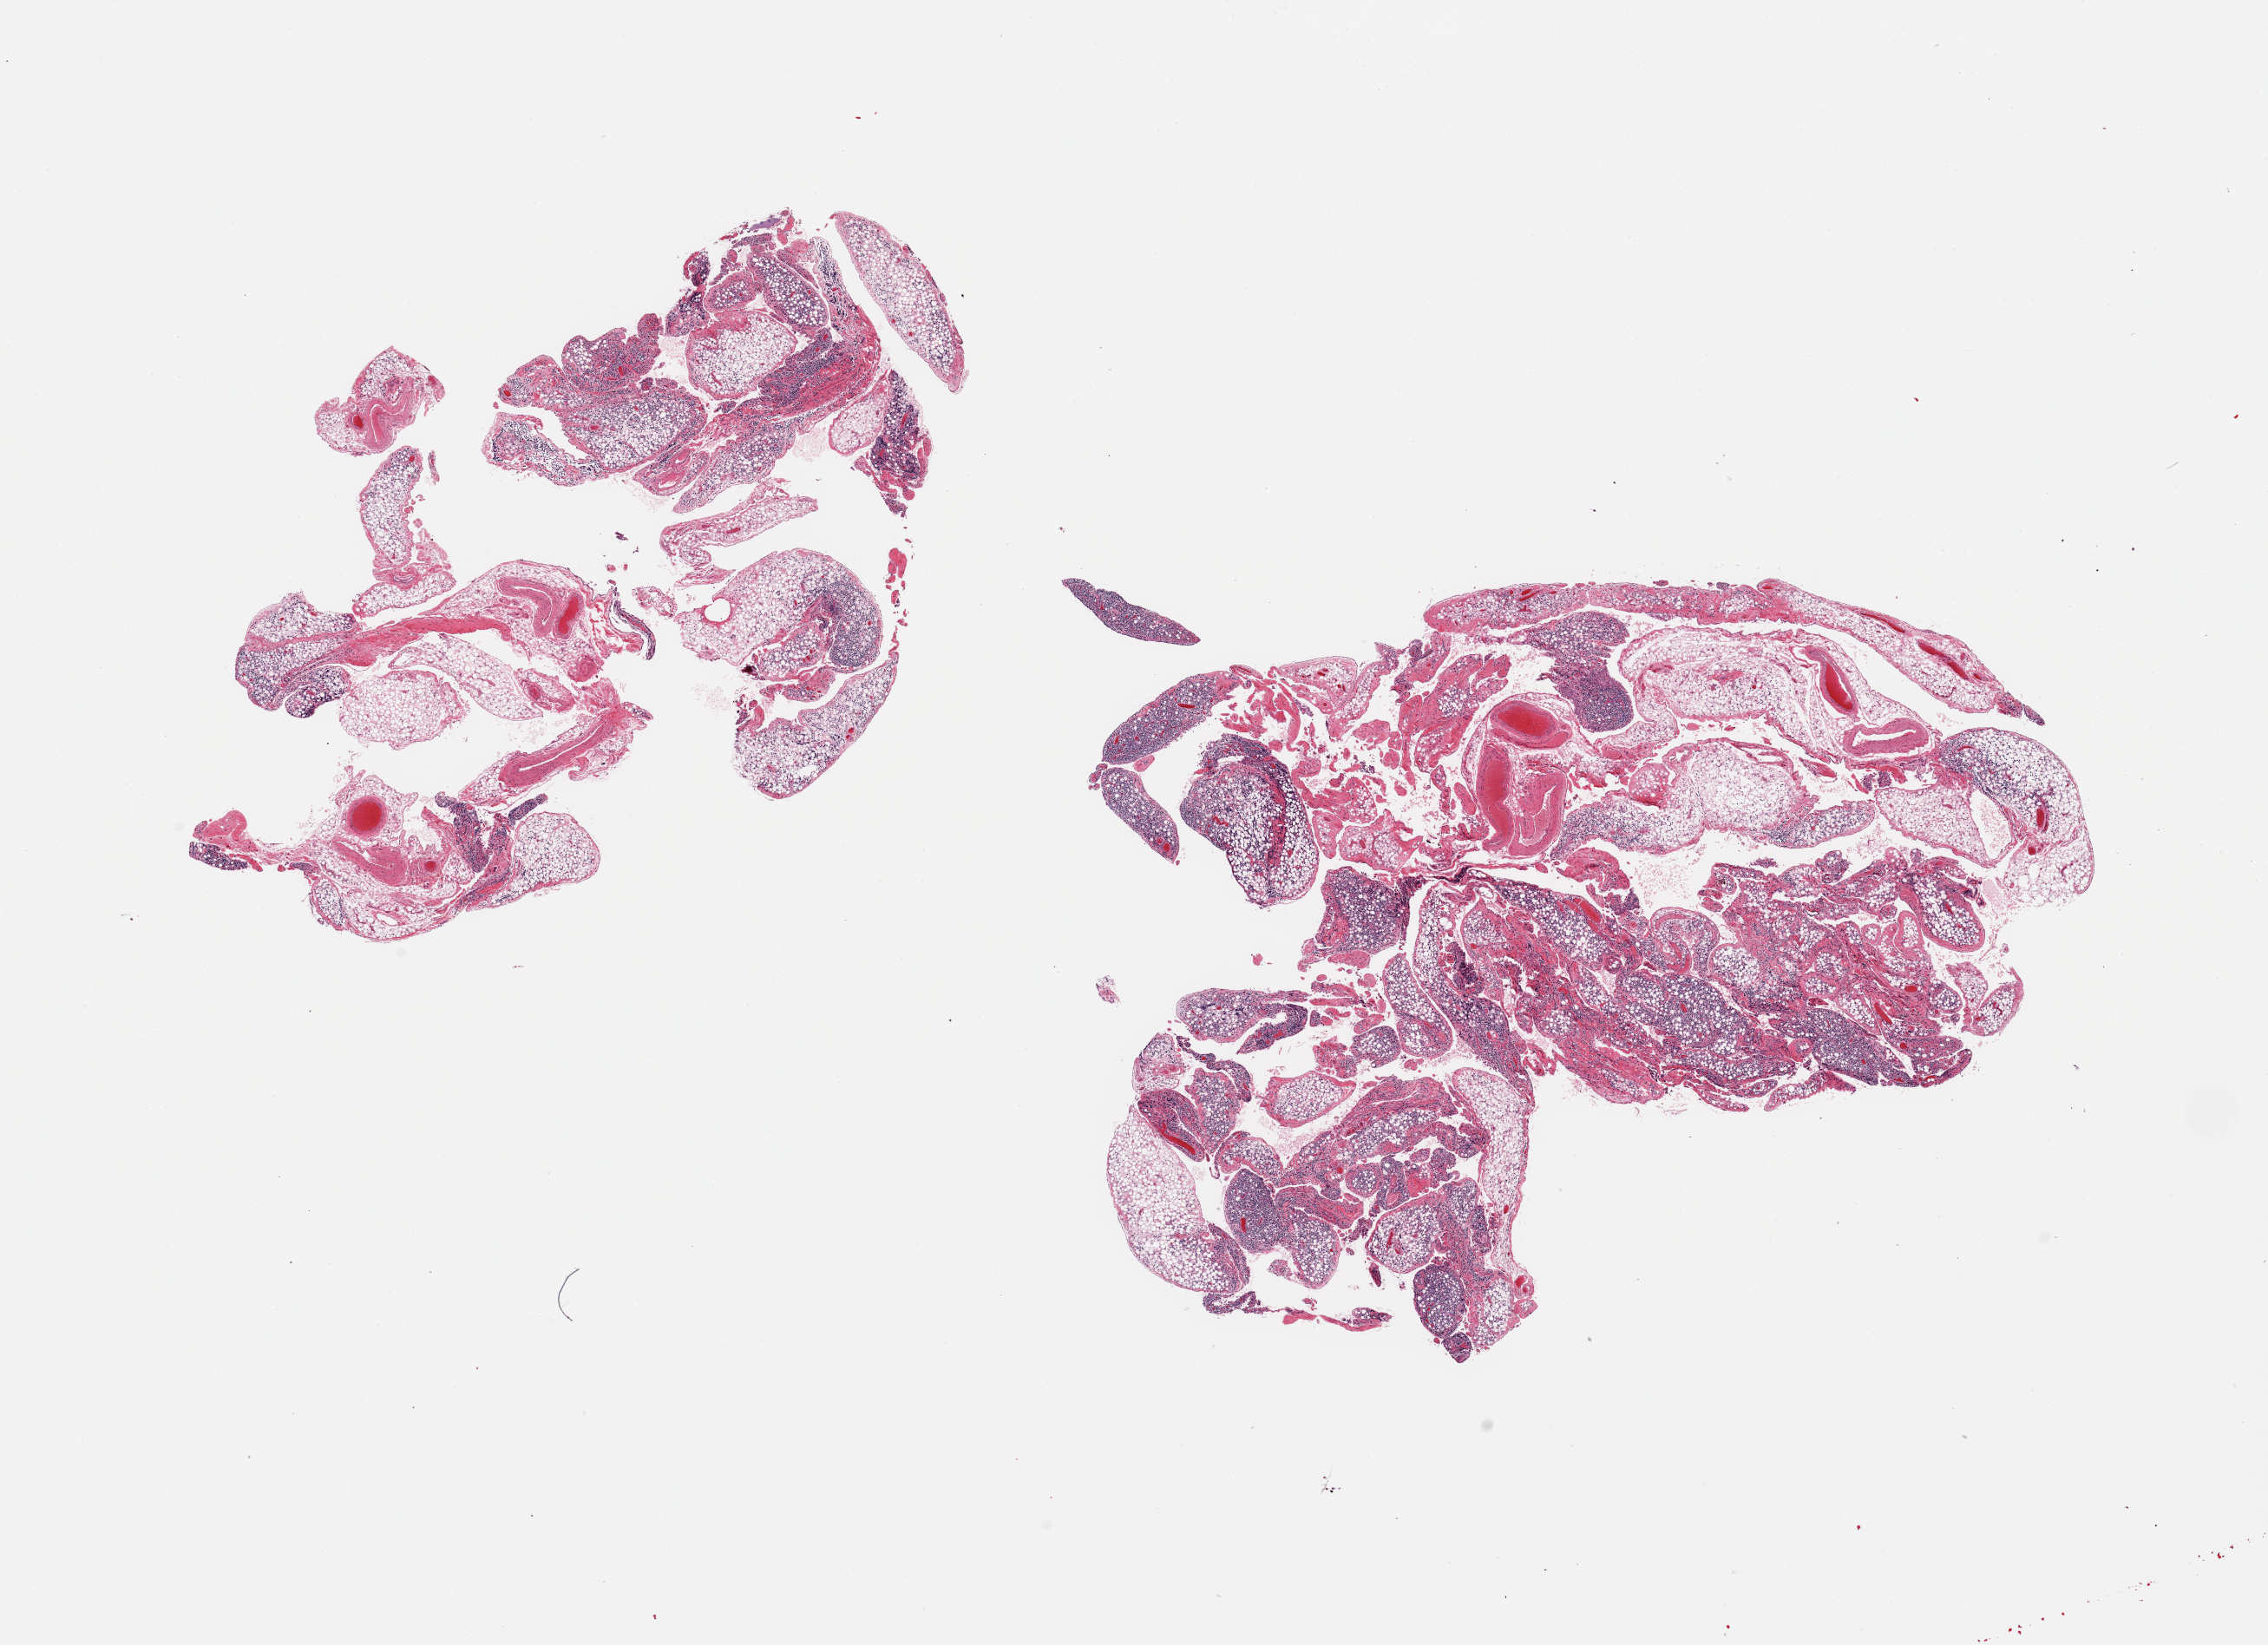
Whole-slide image, hematoxylin and eosin (H&E) stain, whole scanned area (about 20.7 x 15.0 mm, acquisition: 20x scan) shown as a low-resolution overview; PAXgene-fixed paraffin-embedded (PFPE) section; section of omentum (target tissue); tissue donor sample.
Review note (as recorded): 2 pieces; atypical lymphoid infiltrate.